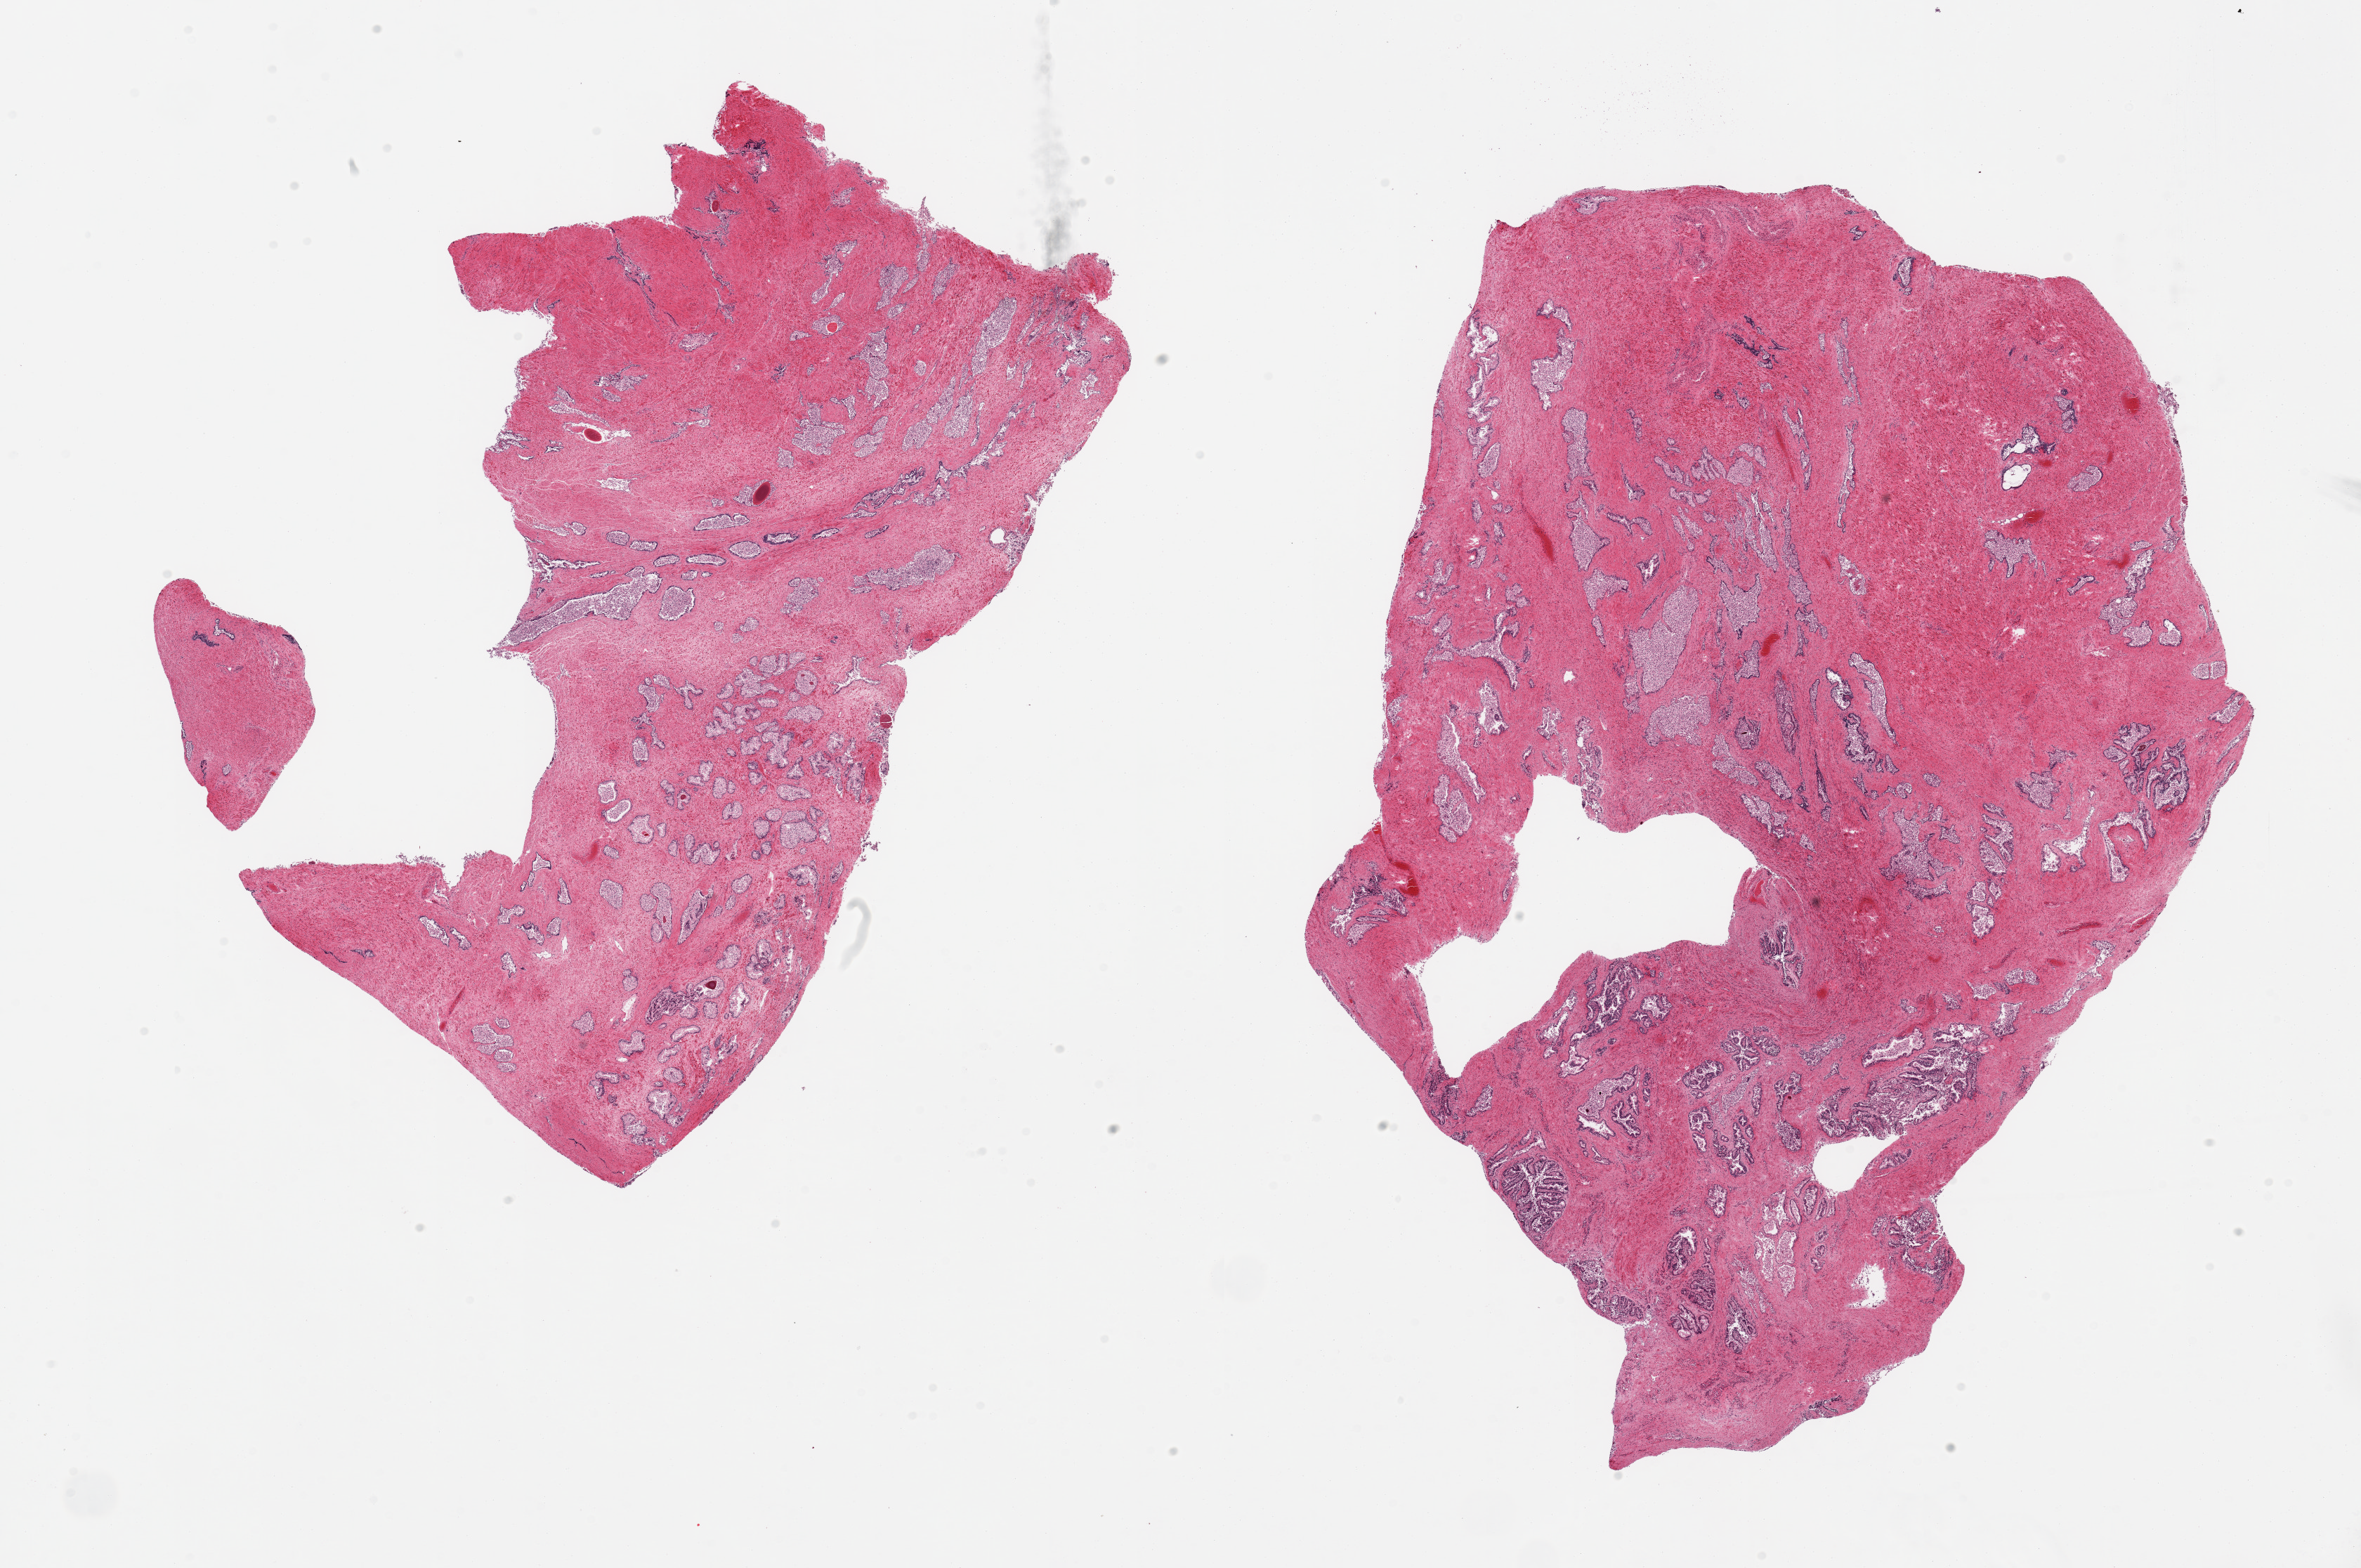
Whole-slide image, hematoxylin and eosin (H&E) stain, shown as a low-resolution overview of the whole scanned area (about 26.6 x 17.7 mm); PAXgene-fixed paraffin-embedded (PFPE) section; sampled site (target tissue): prostate; donor tissue sample. Donor sex: male.
* review note (as recorded): 2 pieces hyperplastic glandular pattern, mucosal epithelium sloughing; basal cells present